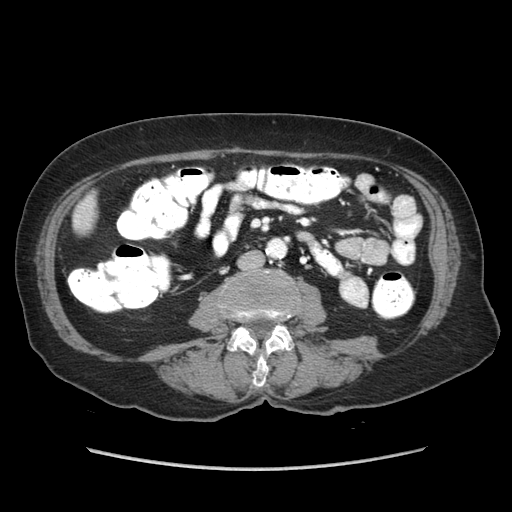
Contrast-enhanced abdominal CT (liver protocol), one axial slice. Slice 6 of 89 in the series (ordered by position). Reconstruction kernel STANDARD. Soft-tissue window (W 400 / L 40 HU). 2.5 mm slice thickness. 512 × 512 image matrix. Case-level facts recorded for this patient, not image findings: diagnosis: hepatocellular carcinoma (patient treated with transarterial chemoembolisation; whether this scan precedes or follows treatment is not stated here); TNM stage (as recorded): Stage-IIIA; Child-Pugh class: A; tumour differentiation: well differentiated; tumour nodularity: multinodular.
Structures marked on this image (semi-automatic segmentation, software-assisted and operator-edited):
- liver parenchyma outside the tumour (the mass and vessels are separate outlines, so this box may not span the whole liver): box from (x=72, y=194) to (x=96, y=232) px